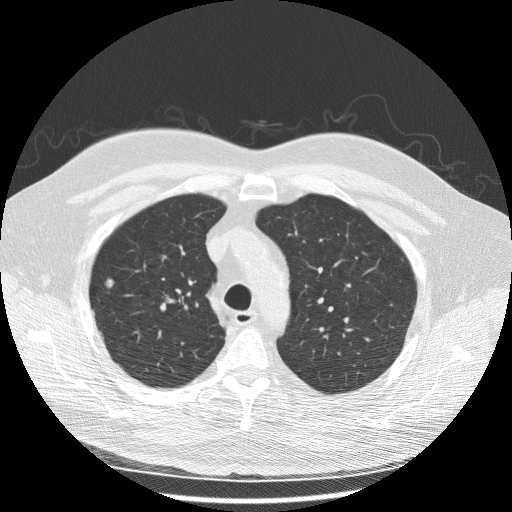
Low-dose screening chest CT, one axial slice; position 186 of 243 along the scan axis; 120 kVp; lung window (W 1500 / L -600 HU); 512 × 512 image matrix, field of view 380 × 380 mm.
Outlined on this slice (manually delineated by an expert):
- lesion 1 (tumor, upper lobe of right lung): box from (x=105, y=278) to (x=115, y=288) px